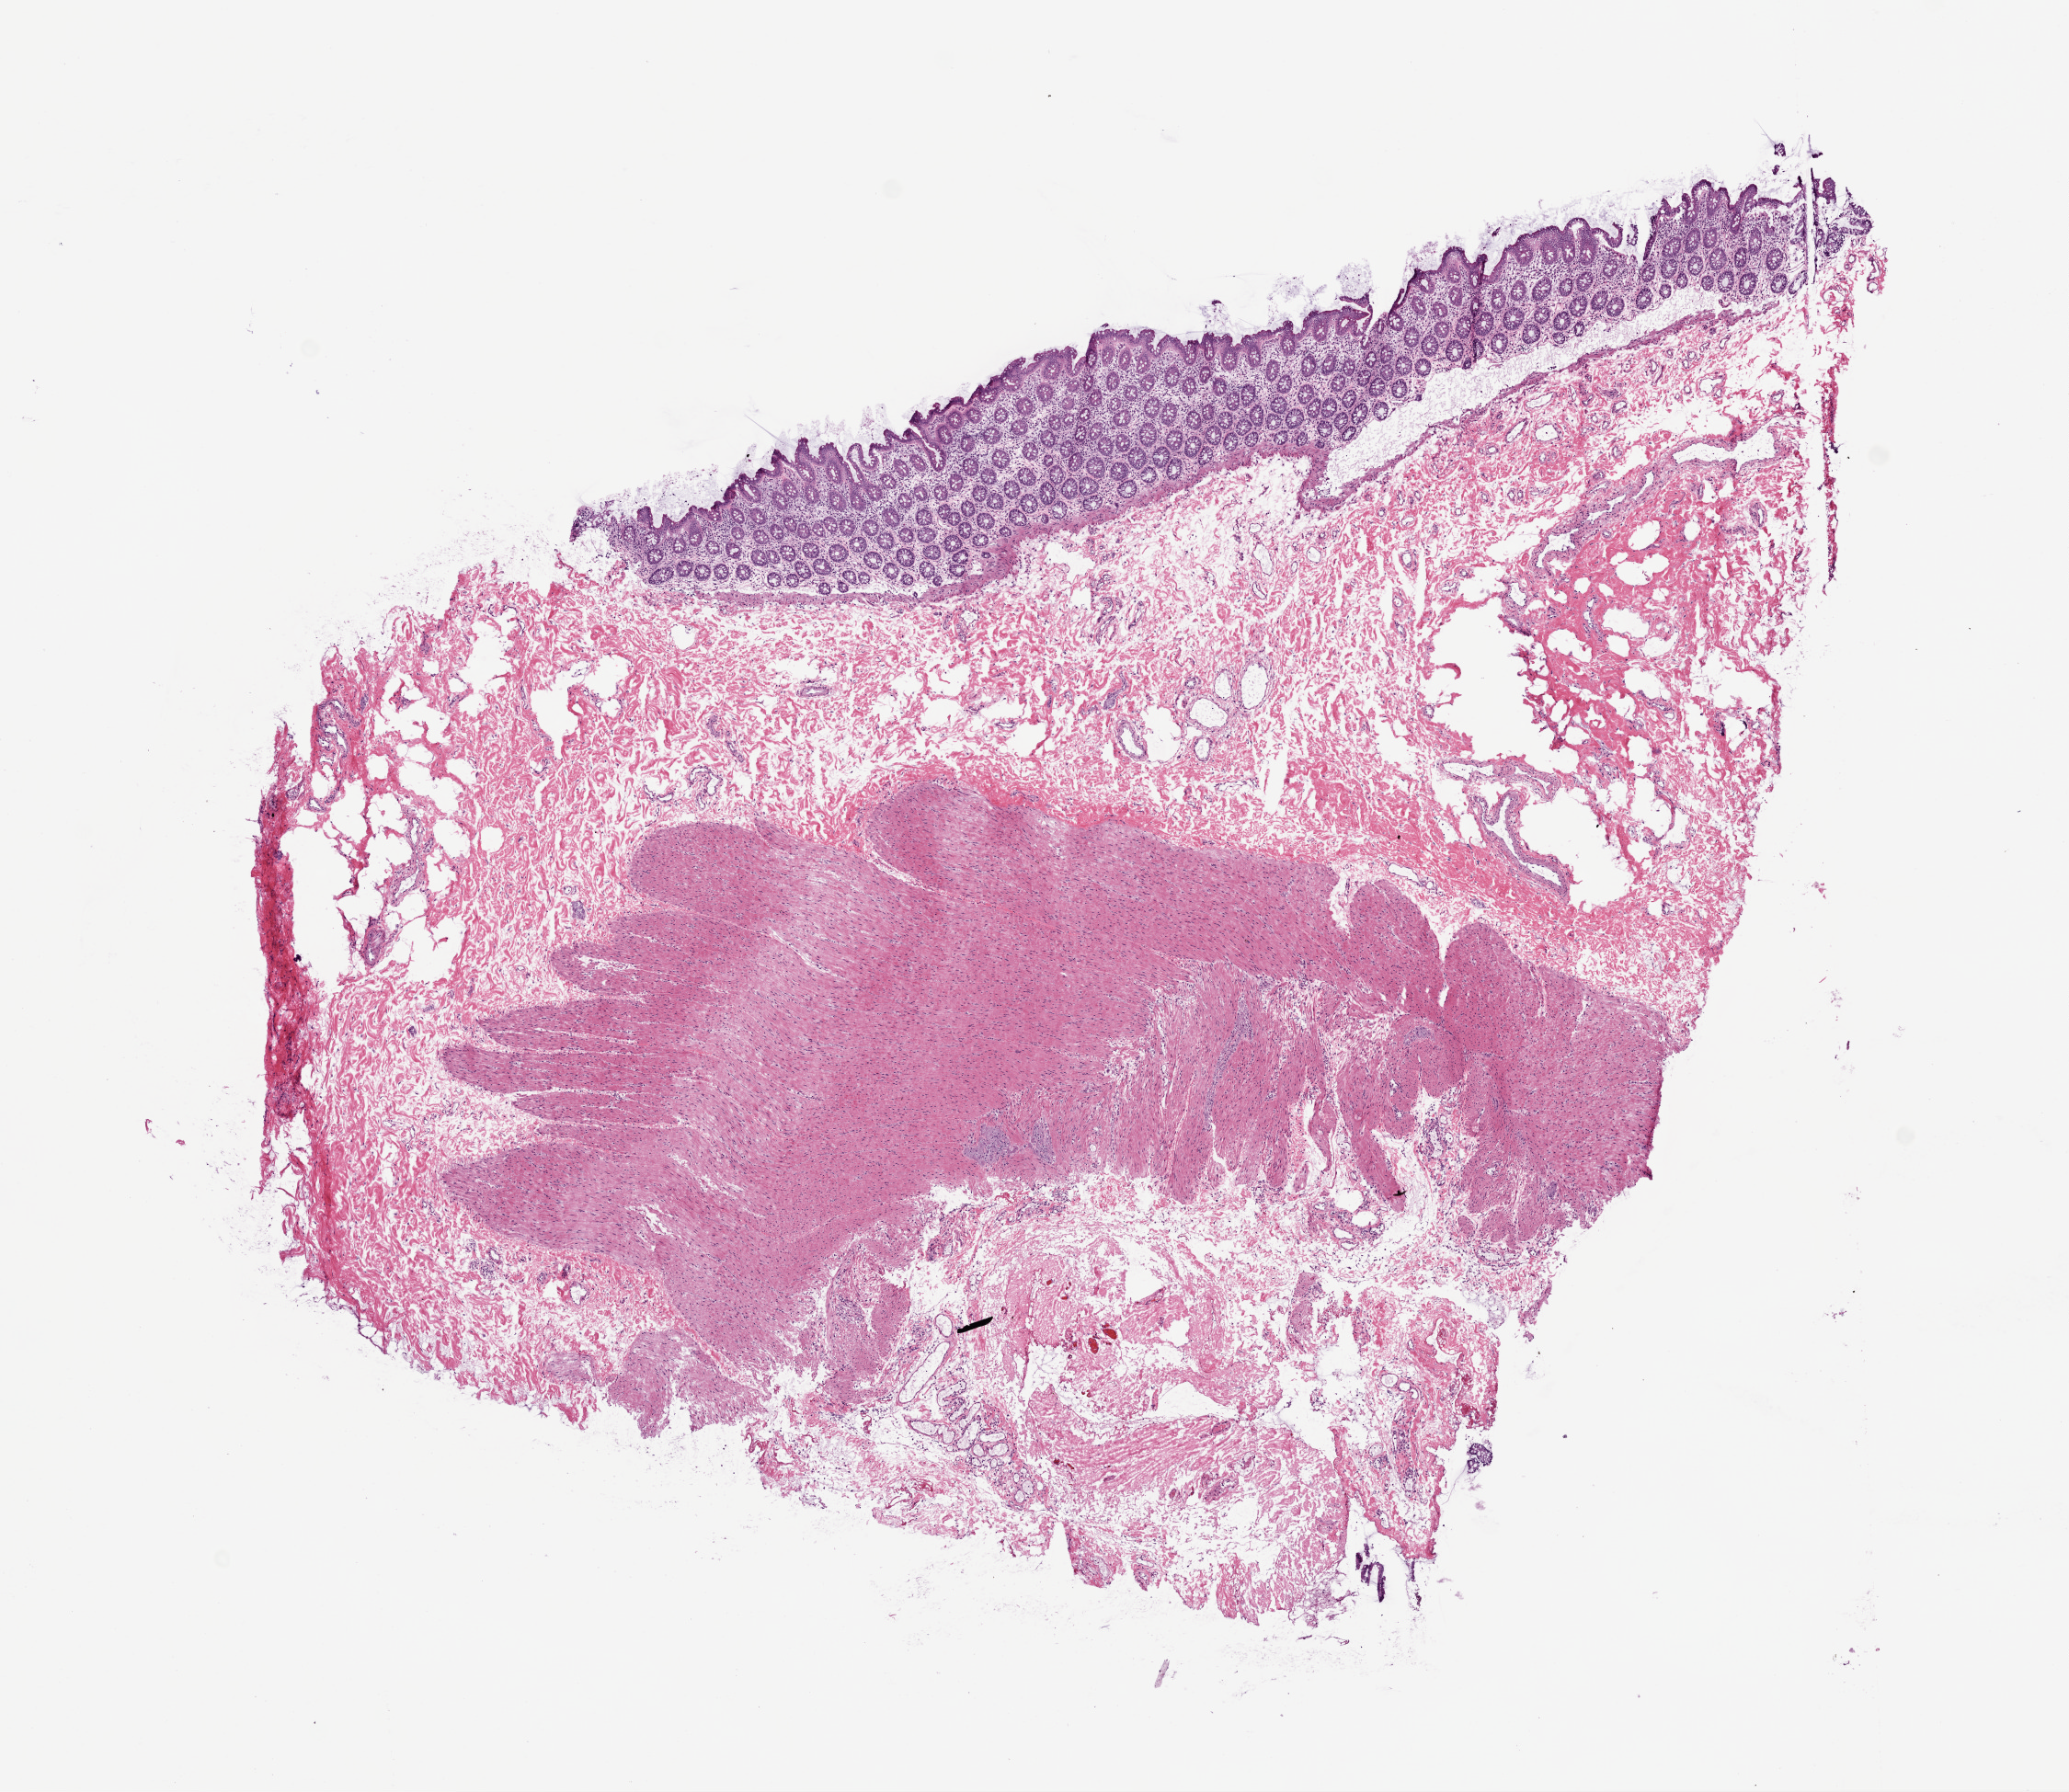
Whole-slide histology image, Hematoxylin and eosin (H&E) stained, a low-resolution overview of the entire scanned area, about 9.0 x 7.8 mm (from a 20x scan). Frozen section from the top of the tissue portion. Sample: solid tissue normal (non-tumour tissue), colon. Patient: male, age at initial diagnosis 46 years.
- this section: solid tissue normal (non-tumour) sample from the same patient
- patient diagnosis: Adenocarcinoma, NOS (splenic flexure of colon)